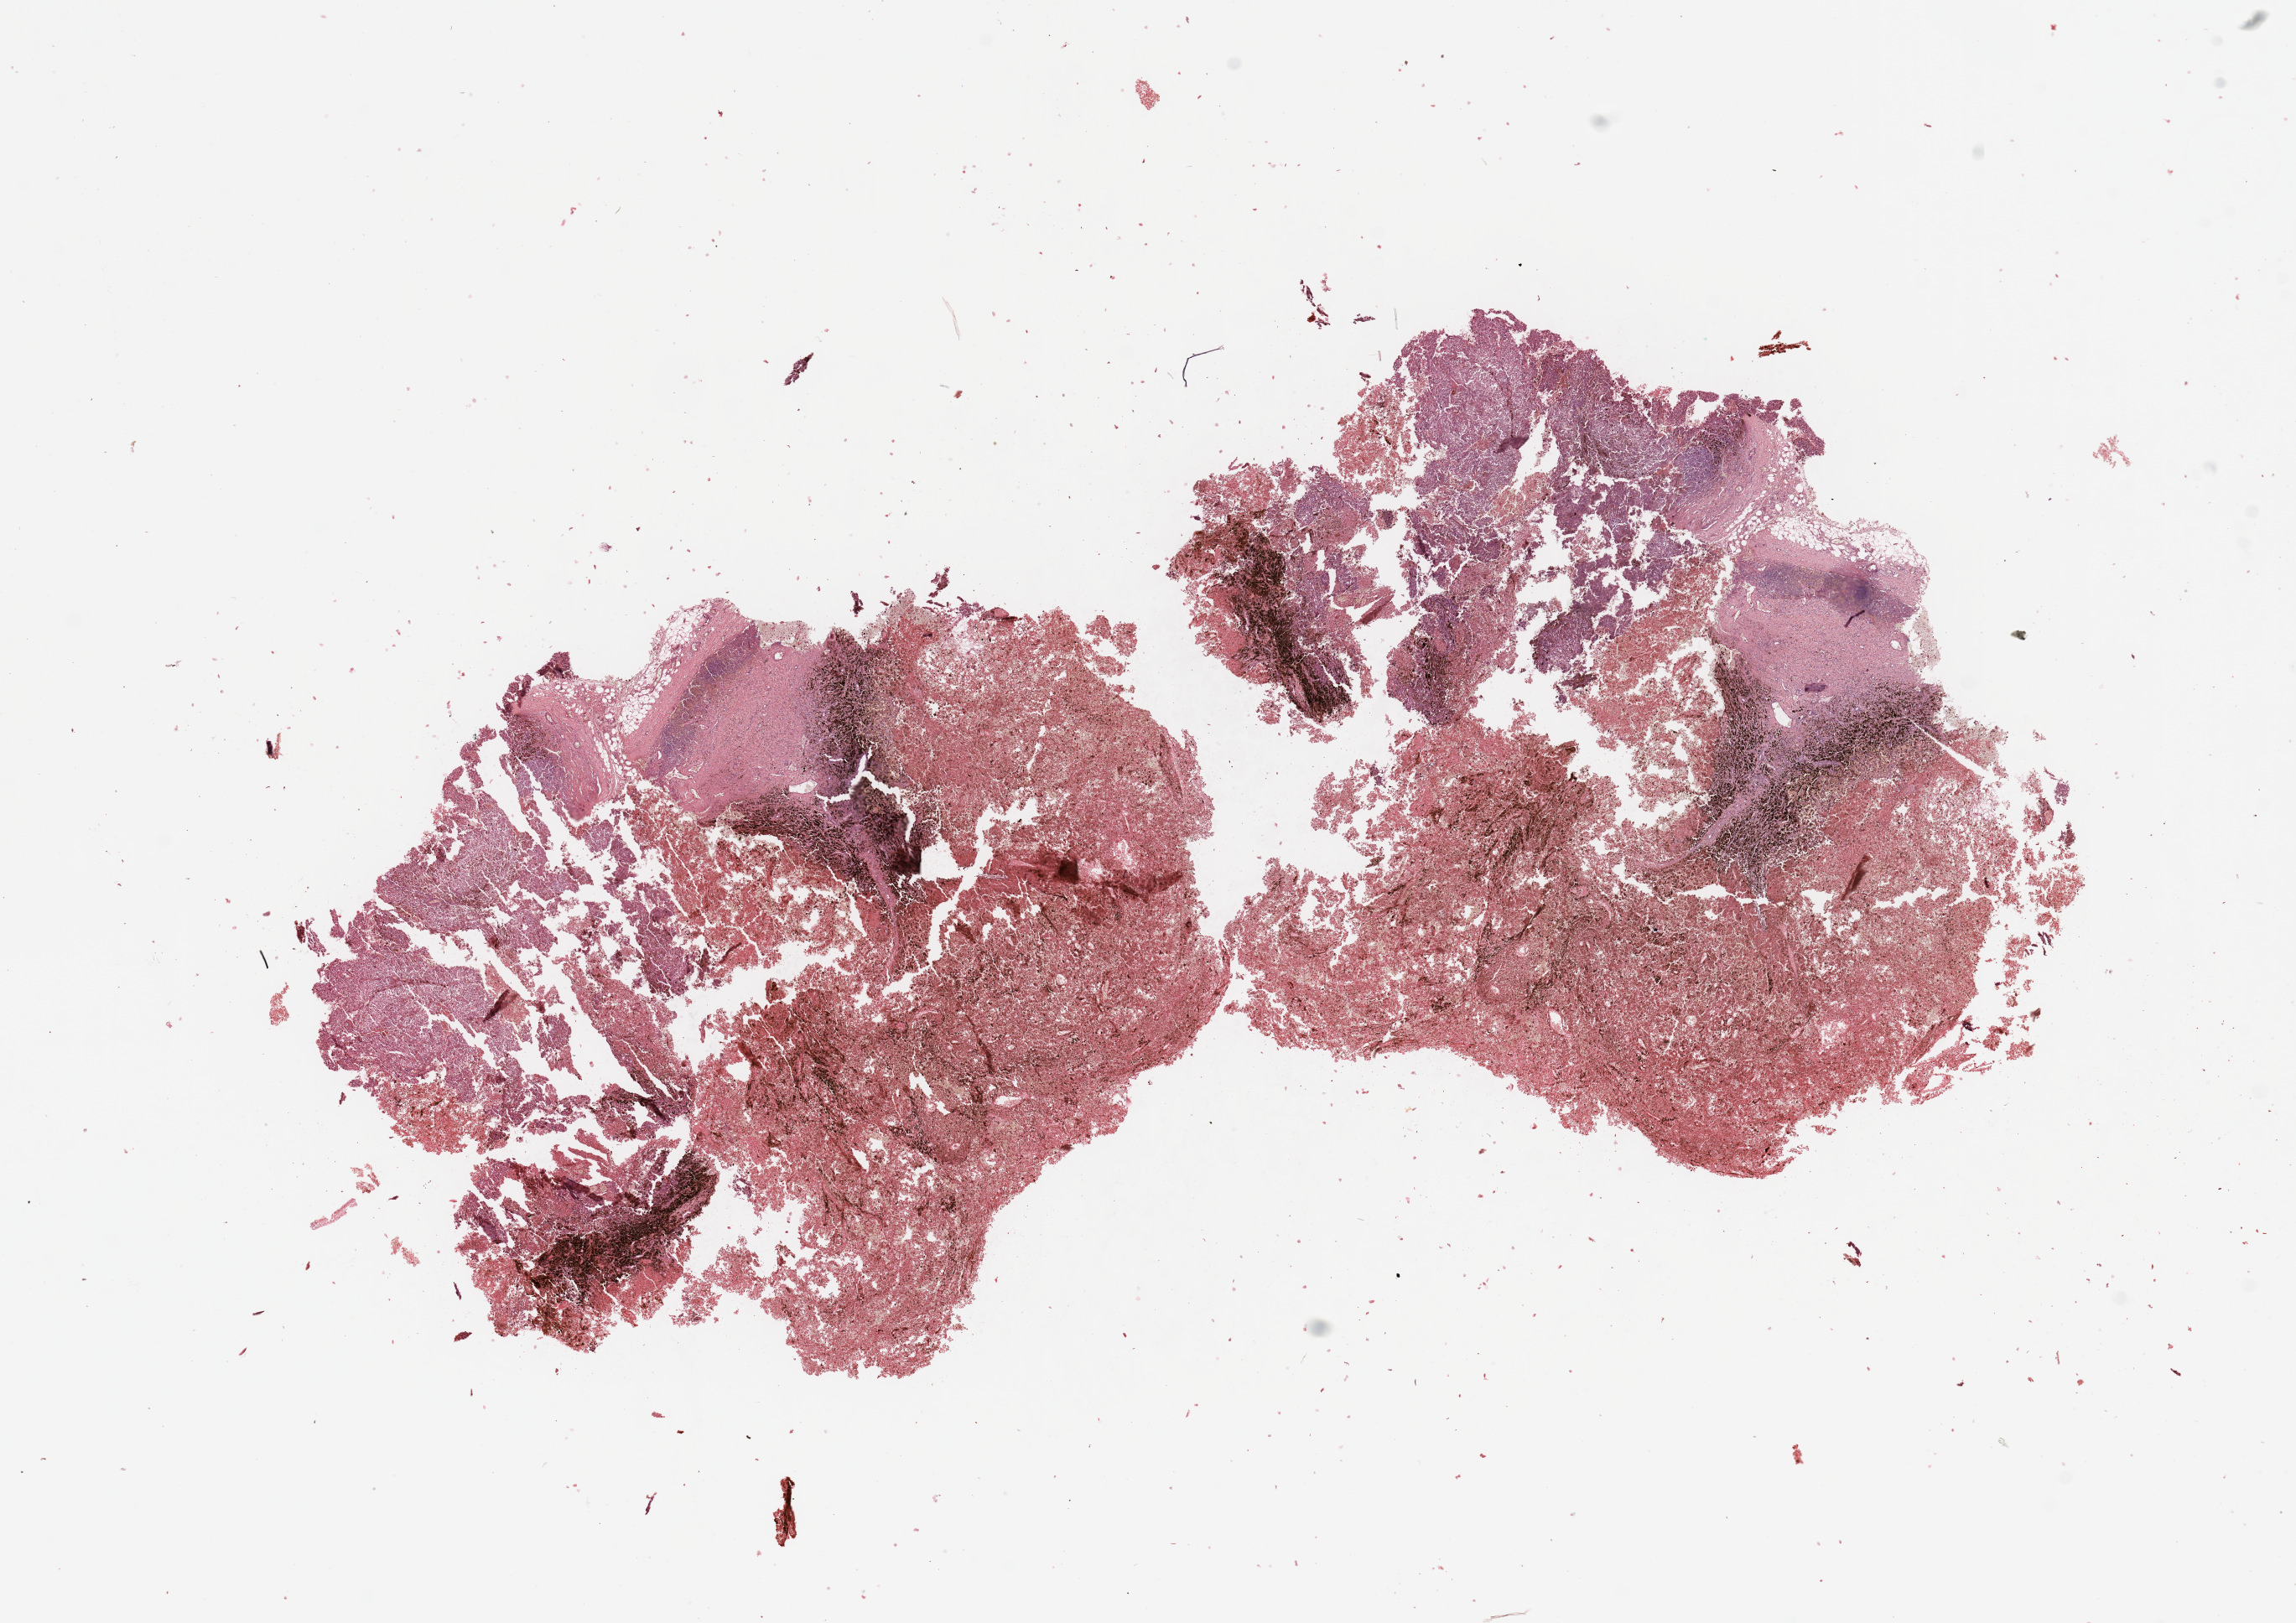
Digitized H&E tissue section (whole slide) — whole scanned area (about 21.7 x 15.3 mm, acquisition: 20x scan) shown as a low-resolution overview. Melanoma tumour tissue; sampled site not recorded. 63-year-old female patient.
- AJCC pathologic stage: IIC
- primary tumour site (as recorded): extremities
- diagnosis: Malignant melanoma, NOS